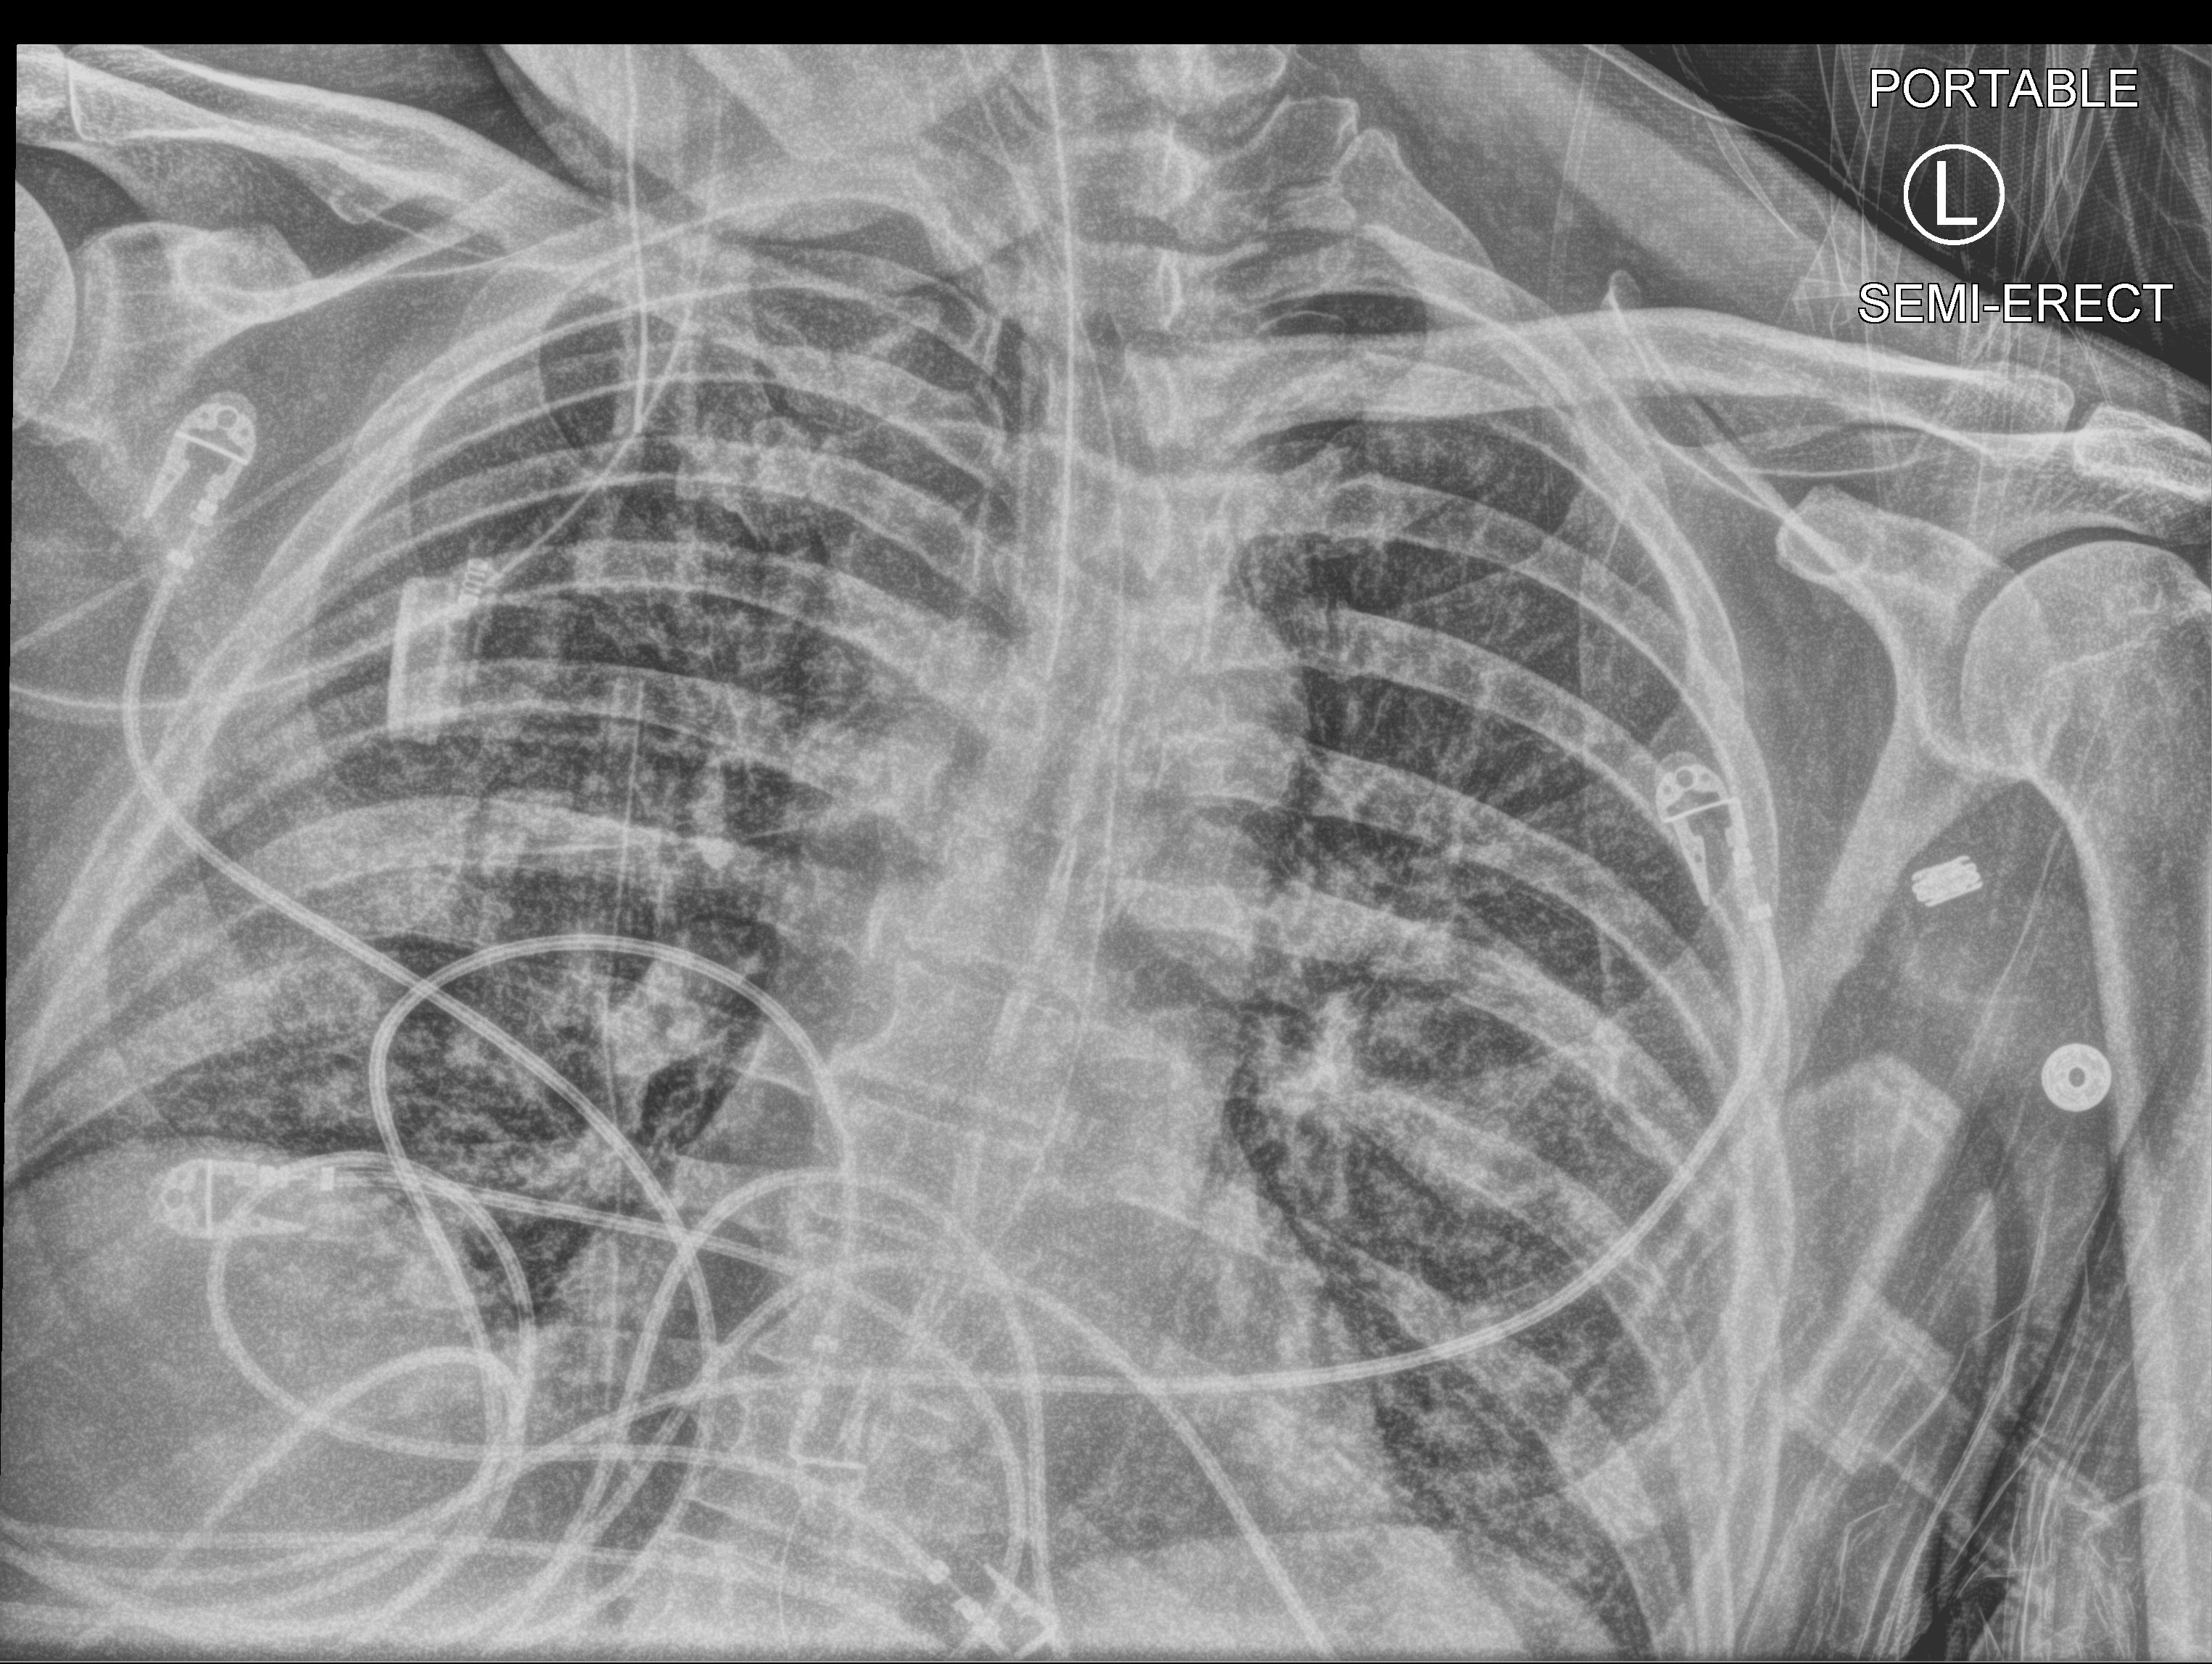
Chest X-ray (portable), anteroposterior (AP) projection. Male patient hospitalised with COVID-19, age 60–74 years.
Hospital-stay facts (about this admission, not read from this image; timing relative to this image not recorded): hypertension (admission record): no; mechanically ventilated during this hospital stay: yes; chronic kidney disease (admission record): no.